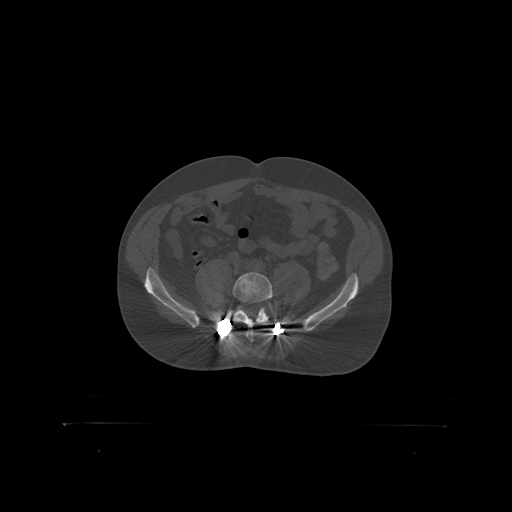
CT including the spine, one axial slice; position 202 of 399 along the scan axis; 120 kVp; bone window (W 1800 / L 400 HU); 512 × 512 image matrix, field of view 650 × 650 mm. Patient: male, 46 years. Case-level facts recorded for this patient, not image findings: primary cancer: skin.
Outlined on this slice (semi-automatically segmented with operator editing):
- L5 vertebra: bounding box [x1, y1, x2, y2] px = [233, 273, 277, 319]